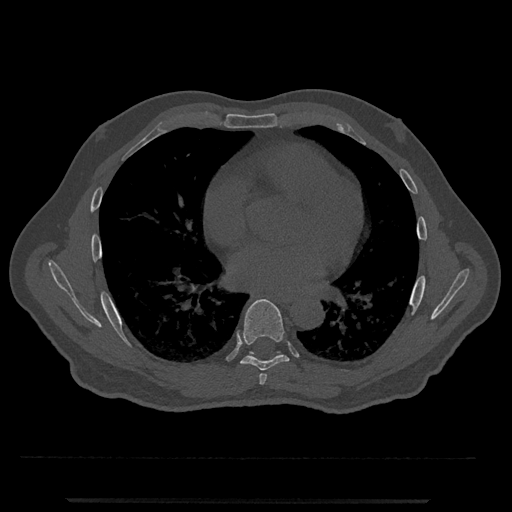
CT including the spine, one axial slice; slice 678 of 797 in the series (ordered by position); reconstruction kernel Br40s/3; bone window (W 1800 / L 400 HU); 0.5 mm slice thickness; 512 × 512 image matrix, field of view 419 × 419 mm. Male patient, age 63 years. Case-level facts recorded for this patient, not image findings: primary cancer: prostate.
Structures marked on this image (semi-automatic segmentation, software-assisted and operator-edited):
- T6 vertebra: bounding box <259,374,267,385> (left, top, right, bottom; pixels)
- T7 vertebra: <236,299,289,371>
- T8 vertebra: <249,351,281,354>